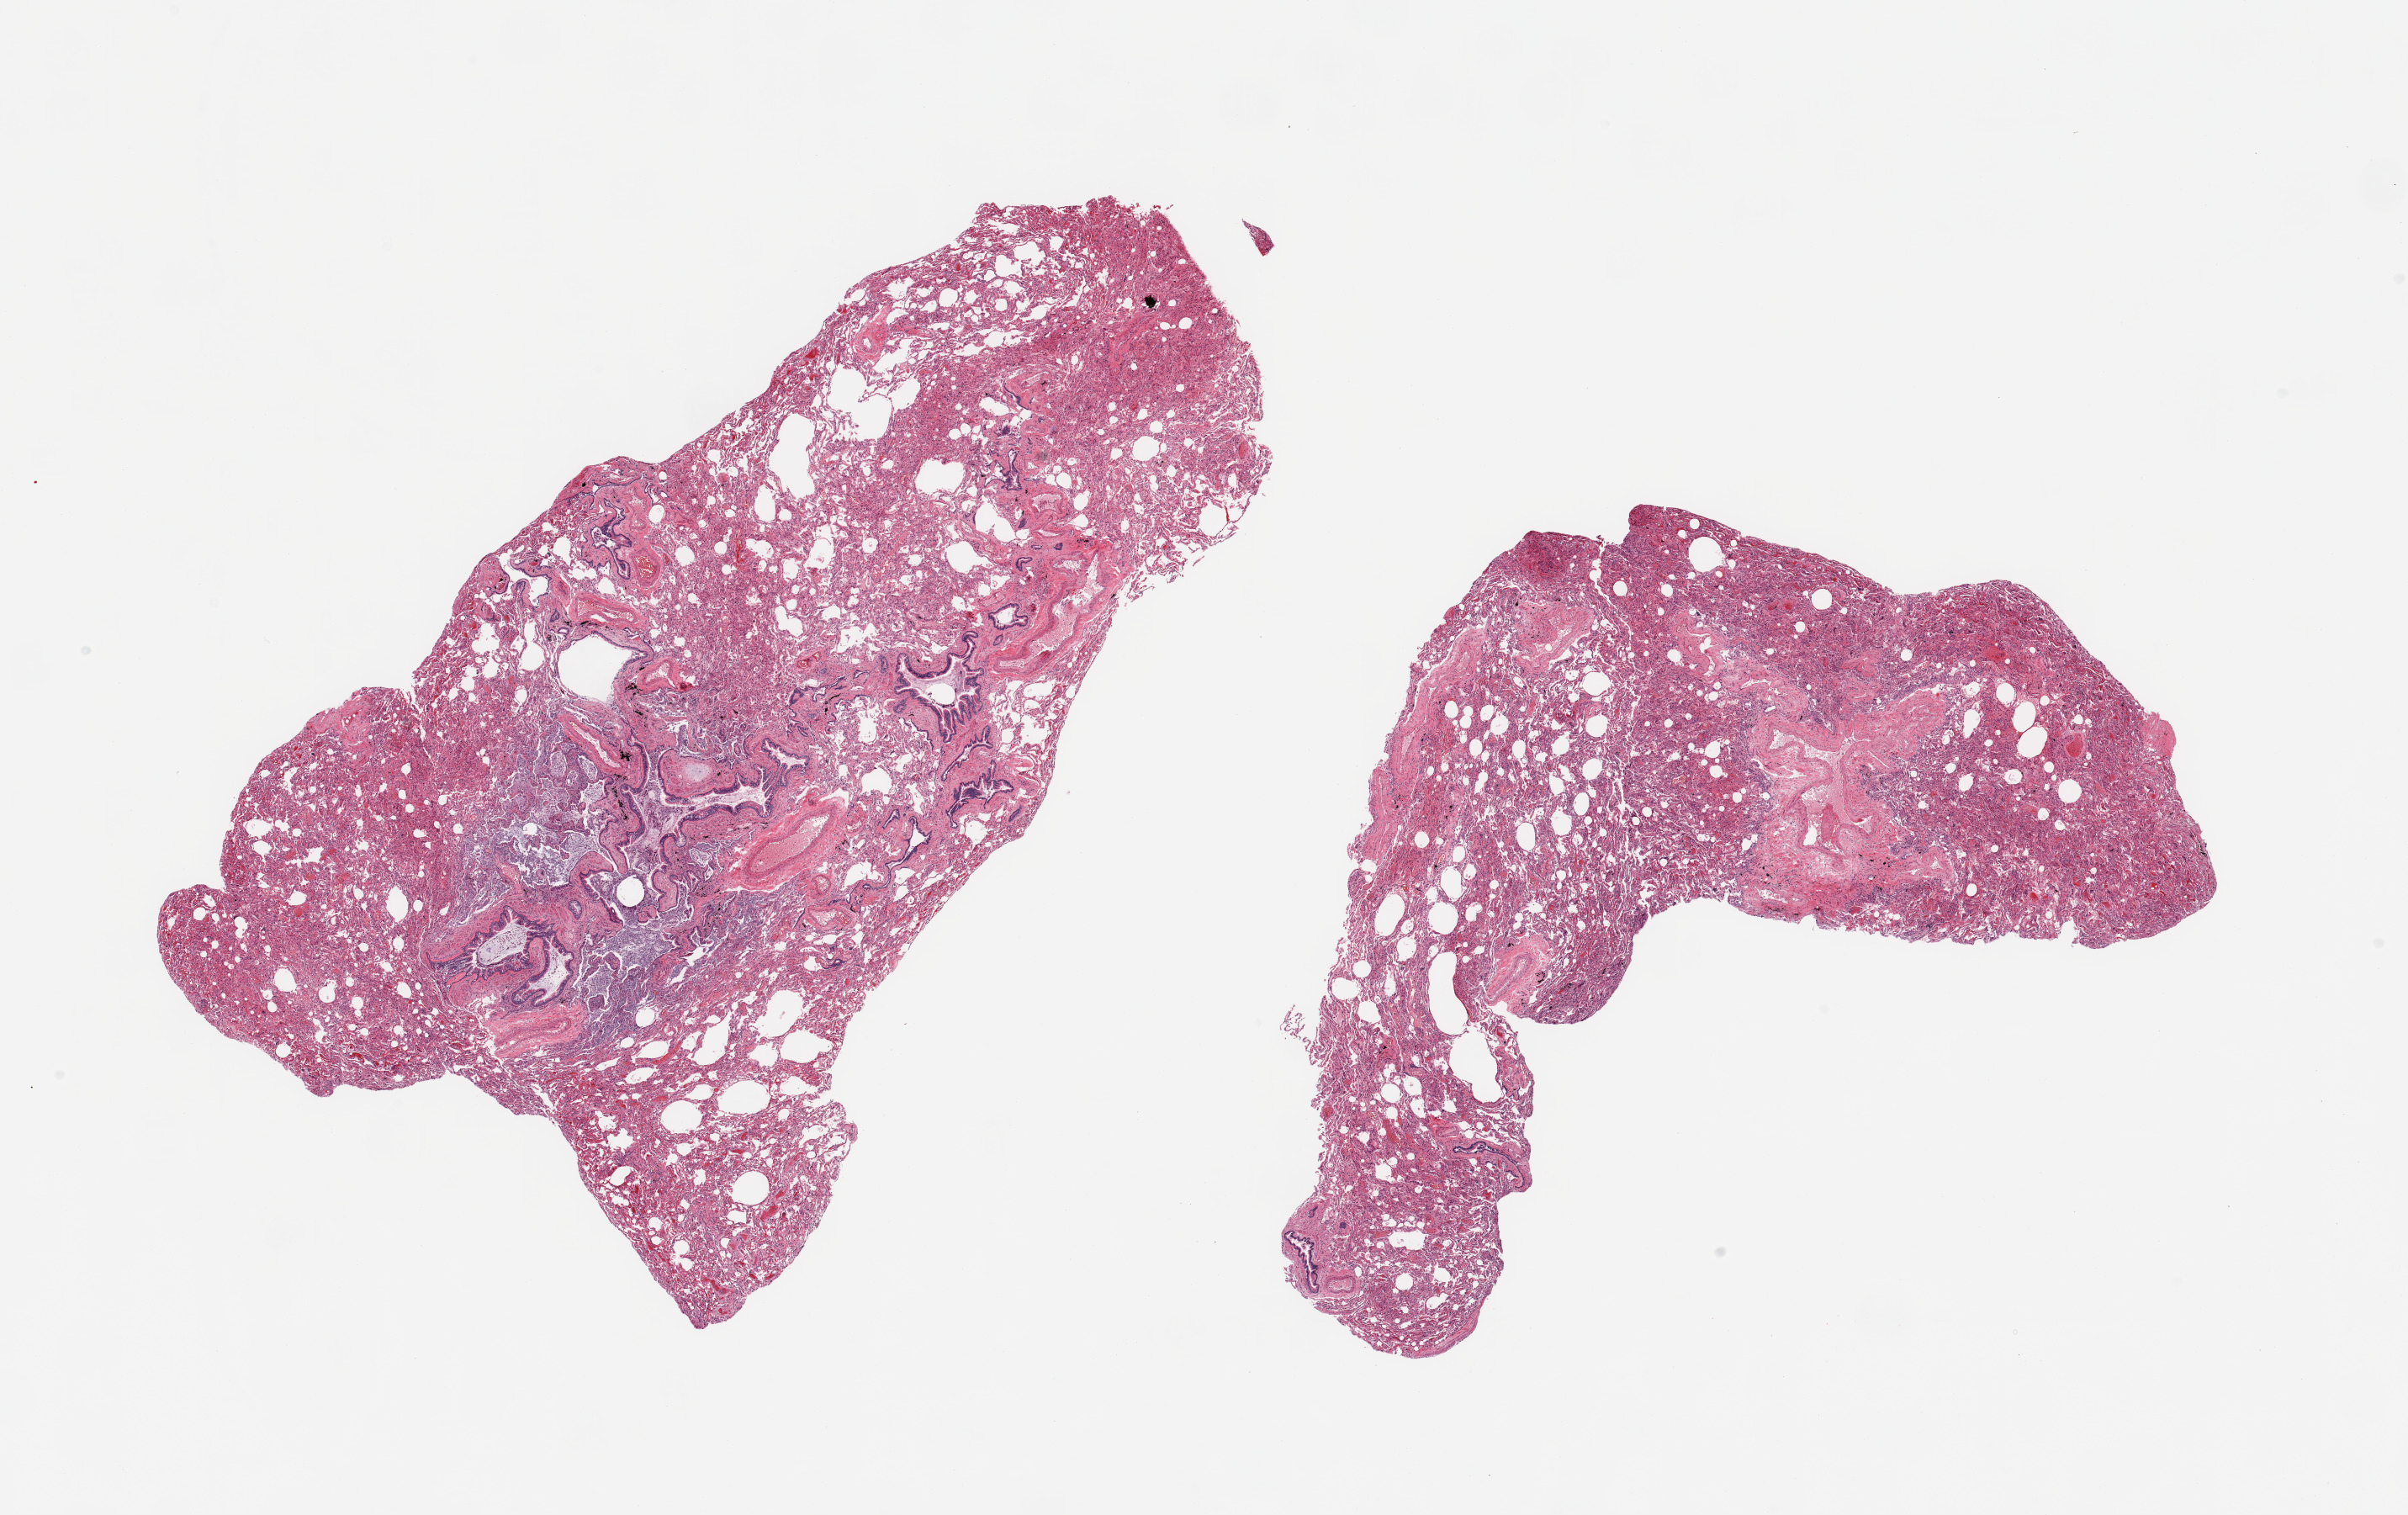
Whole-slide image, haematoxylin and eosin stain, whole scanned area (about 22.6 x 14.2 mm) shown as a low-resolution overview, PAXgene-fixed paraffin-embedded (PFPE) section, section of lung (target tissue), tissue donor sample.
- pathologist's review note for this sample: 2 pieces, moderate congestion/atalectasis